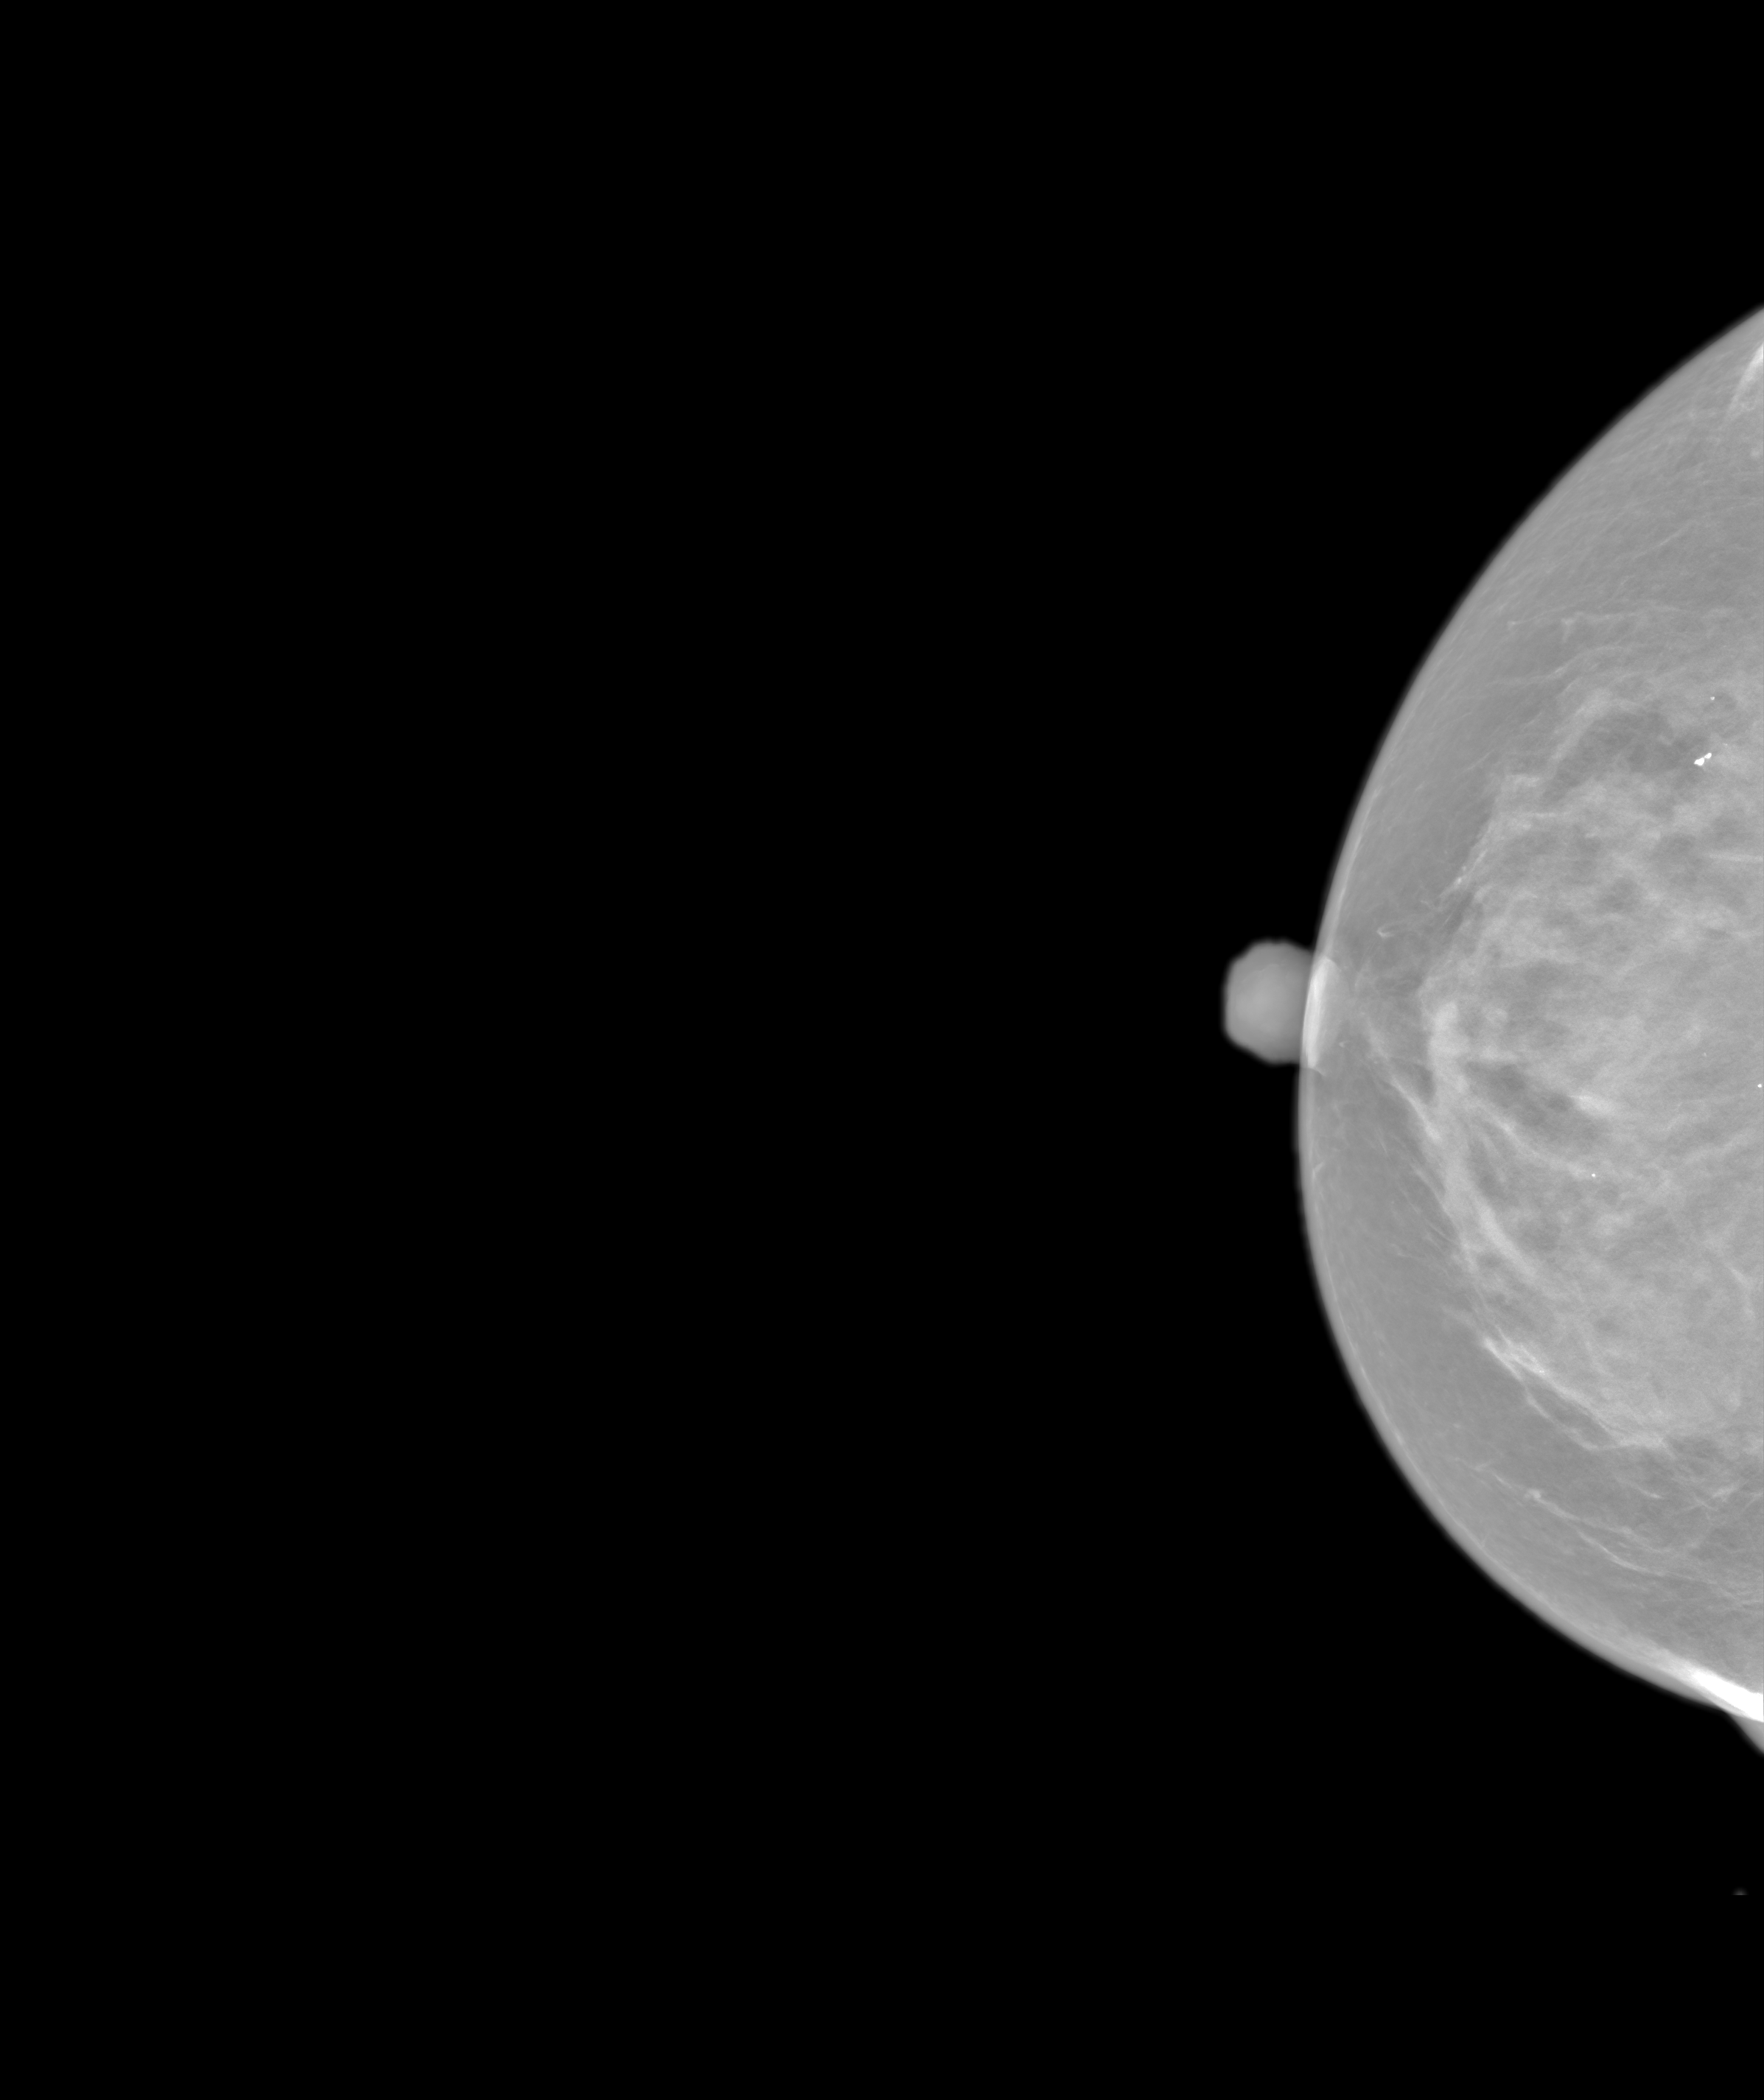
Screening examination.
Image type: synthesized 2-D view from tomosynthesis. Breast: right. Projection: CC view.